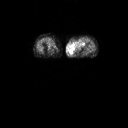
FDG PET of an extremity soft-tissue mass (from a PET/CT study), one axial slice; 3.27 mm slice thickness; 128 × 128 image matrix, field of view 700 × 700 mm. Patient: female, 74 years. From the clinical record (not read from this slice): histological type: pleomorphic leiomyosarcoma; grade: high; site of the primary tumour: left thigh.
Structures marked on this image (expert contour drawn on MRI and transferred to this co-registered scan by the dataset authors):
- gross tumour volume including surrounding oedema: box from (x=70, y=40) to (x=86, y=53) px
- gross tumour volume (mass): (x=70, y=48)–(x=75, y=53)